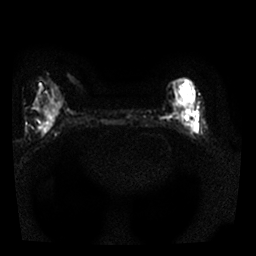
Breast MRI, one axial slice; position 10 of 25 along the scan axis; diffusion-weighted series; image 2 of 4 stored at this slice position (different b-values; order by instance number); 1.5 T; 256 × 256 image matrix, field of view 300 × 300 mm. Female patient.
Structures marked on this image (manually delineated by an expert):
- tumour on diffusion-weighted imaging: bounding box <181,109,197,130> (left, top, right, bottom; pixels)